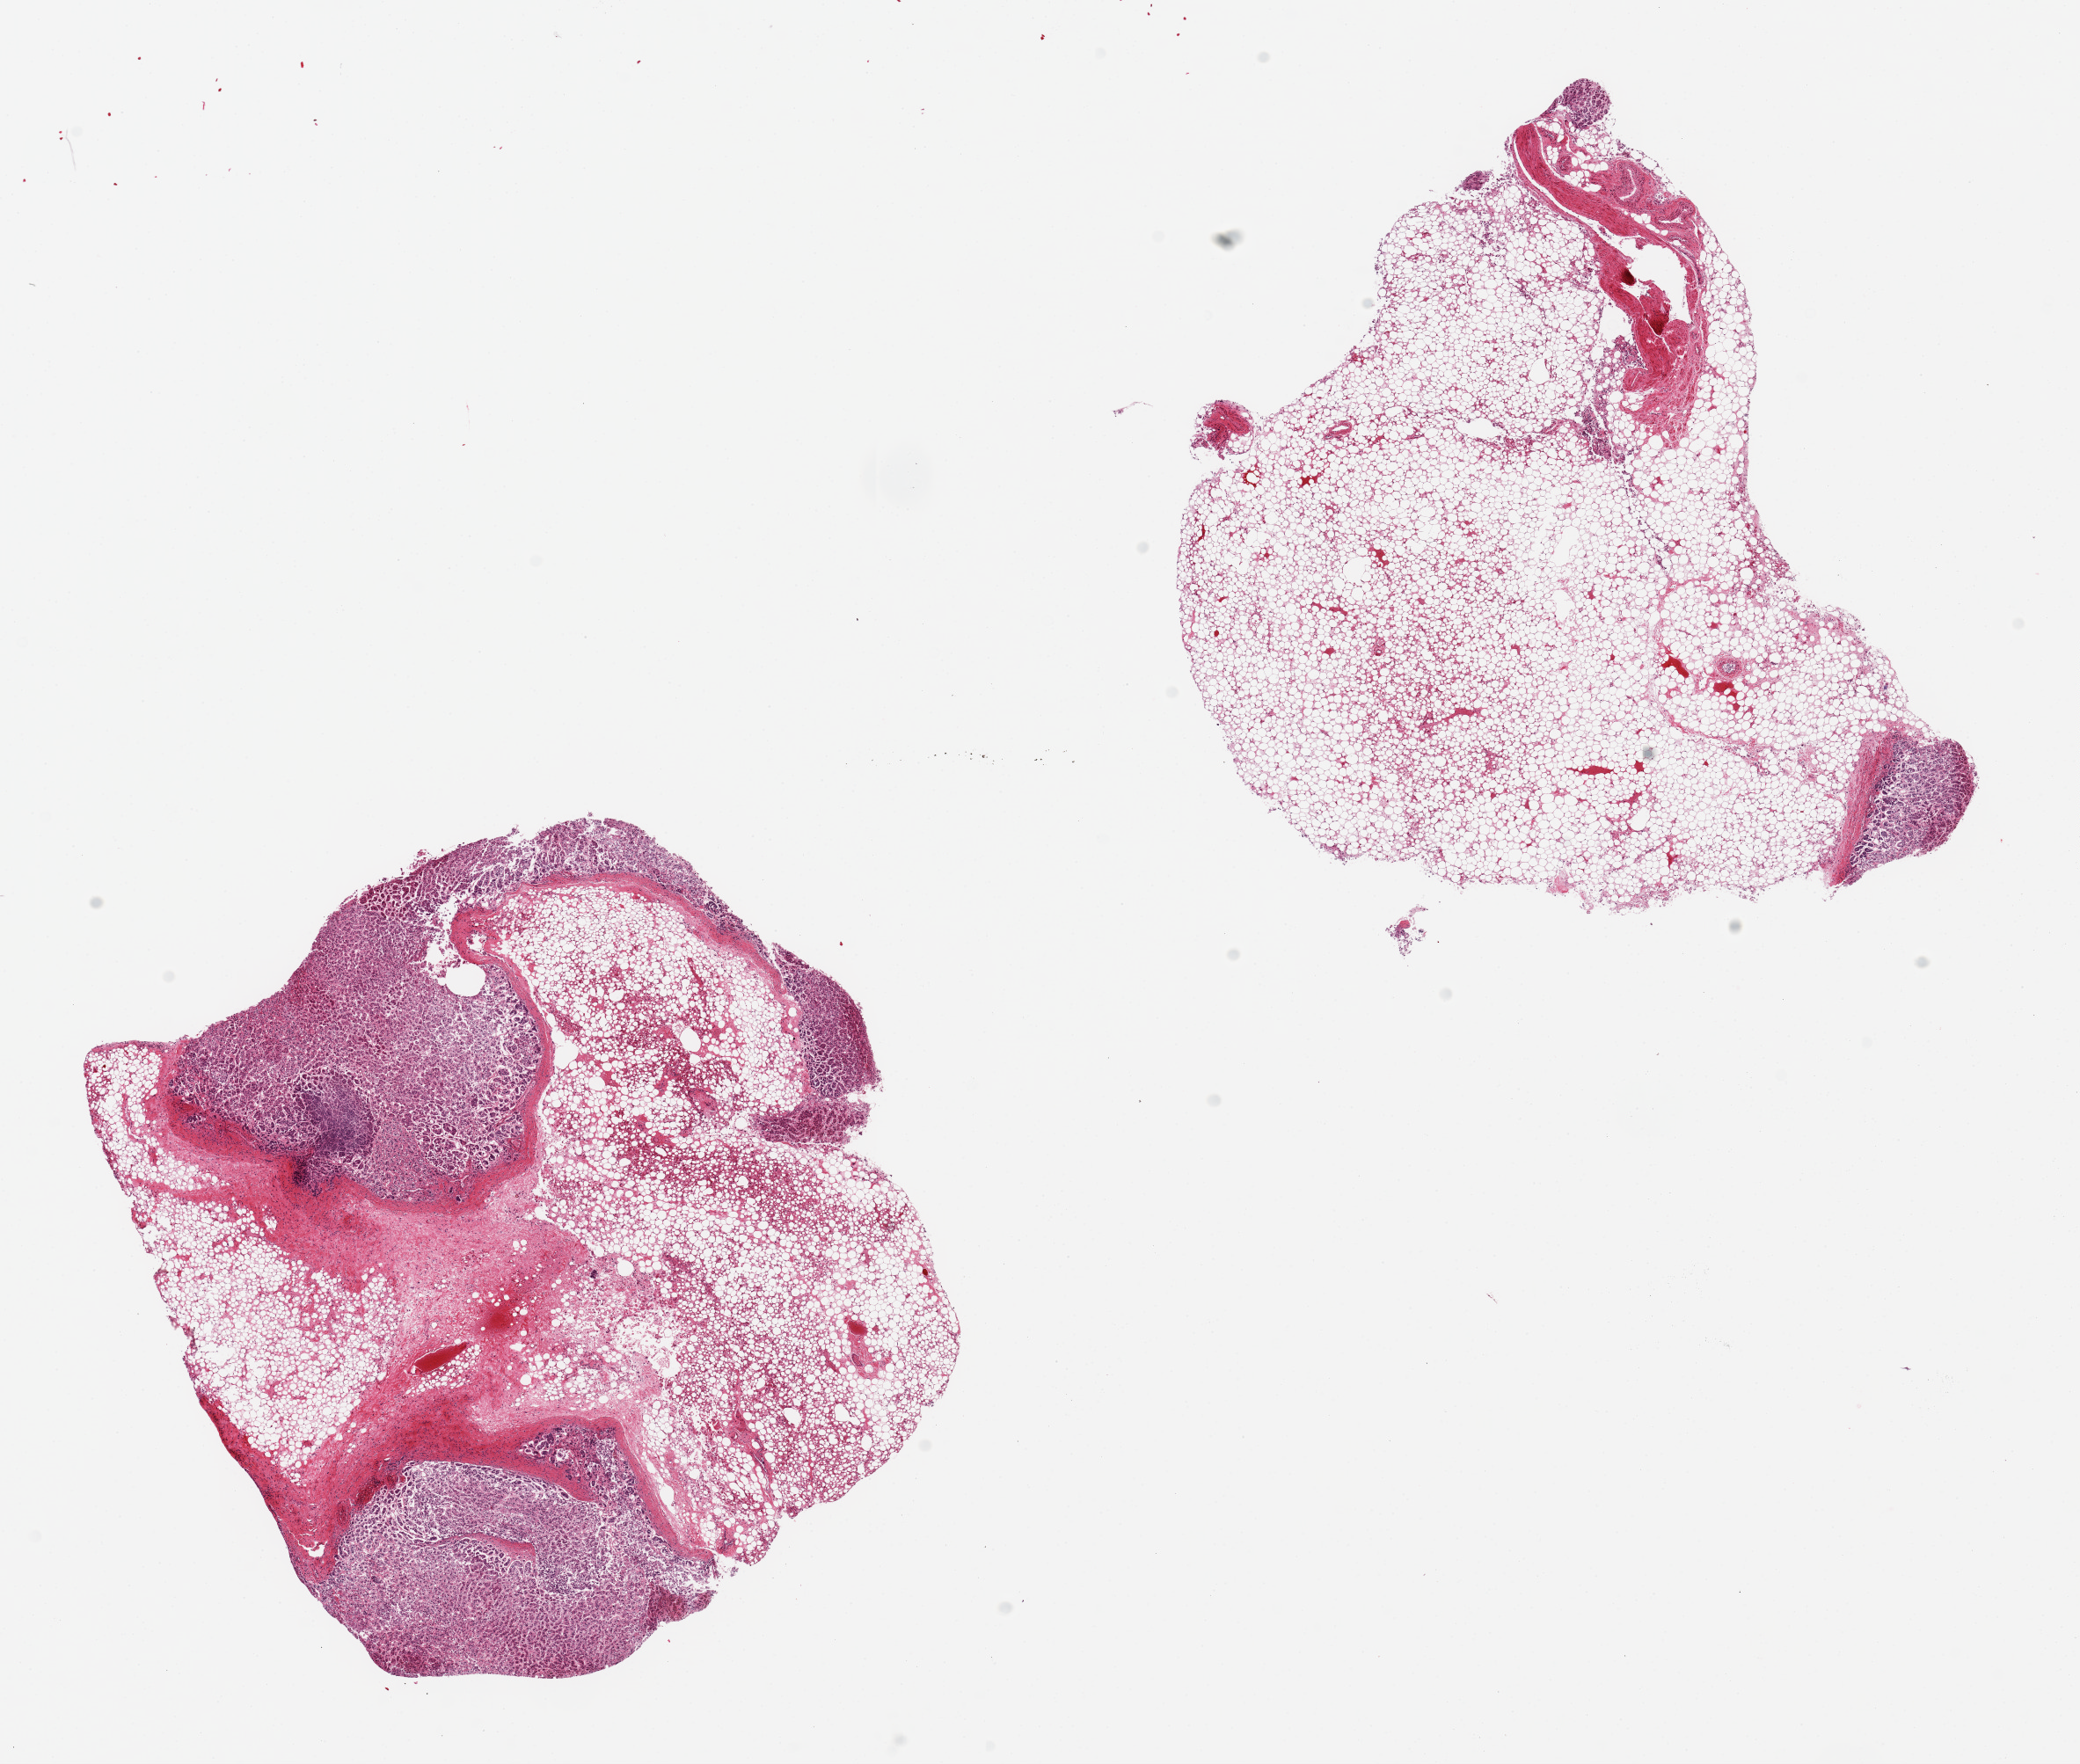
Whole-slide image, H&E stain, brightfield — whole scanned area (about 18.7 x 15.9 mm) shown as a low-resolution overview, PAXgene-fixed paraffin-embedded (PFPE) section, target tissue: adrenal gland, donor tissue sample. Male donor.
Review note (as recorded): 2 pieces, 7x6.5 & 7.5x6mm; 1, 60% adipose; other >90% adipose.